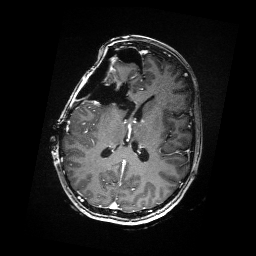
Brain MRI from a brain-tumour surgery series, one axial slice. Slice 81 of 176 in the series (ordered by position). T1-weighted post-contrast. 256 × 256 image matrix. From the clinical record (not read from this slice): histopathology: Metastatic Carcinoma from Breast primary; tumour location: Right Frontal.
Structures marked on this image (manually delineated by an expert):
- residual tumour: bounding box [x1, y1, x2, y2] px = [89, 68, 116, 103]